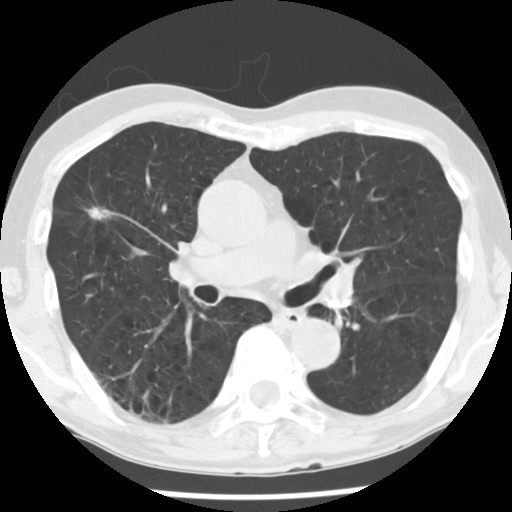
Axial slice from a low-dose chest CT screening exam, baseline screening round, lung window (W 1500 / L -600 HU), standard (soft-tissue) reconstruction kernel (STANDARD), 512 × 512 image matrix, field of view 309 × 309 mm. Male participant, aged 72 years at enrolment. Current smoker at enrolment.
• Expert reader's lesion annotation, box from (x=77, y=196) to (x=132, y=239) px.
• Reader record for this screening exam (exam-level; its link to the box is not recorded): non-calcified nodule or mass ≥4 mm, right upper lobe, 11 × 8 mm, spiculated (stellate) margins, soft tissue attenuation.
• Official screen result: positive, change unspecified: nodule(s) >= 4 mm or enlarging nodule(s), mass(es), or other non-specific abnormalities suspicious for lung cancer.
• Later outcome: lung cancer diagnosed 72 days after this screen — bronchiolo-alveolar adenocarcinoma, NOS, right upper lobe, moderately differentiated (G2), stage IA (AJCC 6th edition), 10 mm at pathology.